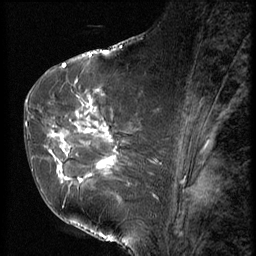
Breast MRI (dynamic contrast-enhanced), one sagittal slice. Slice 33 of 56 in the series (ordered by position). 3 images stored at this slice position (order not interpretable as contrast timing). 1.5 T. TE 4.2 ms, TR 9 ms. 2.5 mm slice thickness. 256 × 256 image matrix. Female patient, age 61 years. Case-level facts recorded for this patient, not image findings: setting: breast cancer imaged before/during neoadjuvant chemotherapy; receptor status: HR-positive, HER2-negative.
Outlined on this slice (semi-automatic segmentation, software-assisted and operator-edited):
- analysis volume of interest (the breast-tissue region the enhancement analysis was run in; not a lesion): bounding box (x1, y1, x2, y2) in pixels: (47, 89, 153, 191)
- tumour enhancement mask (voxels above the 140 % enhancement threshold inside the analysis volume of interest): (53, 103, 115, 182)